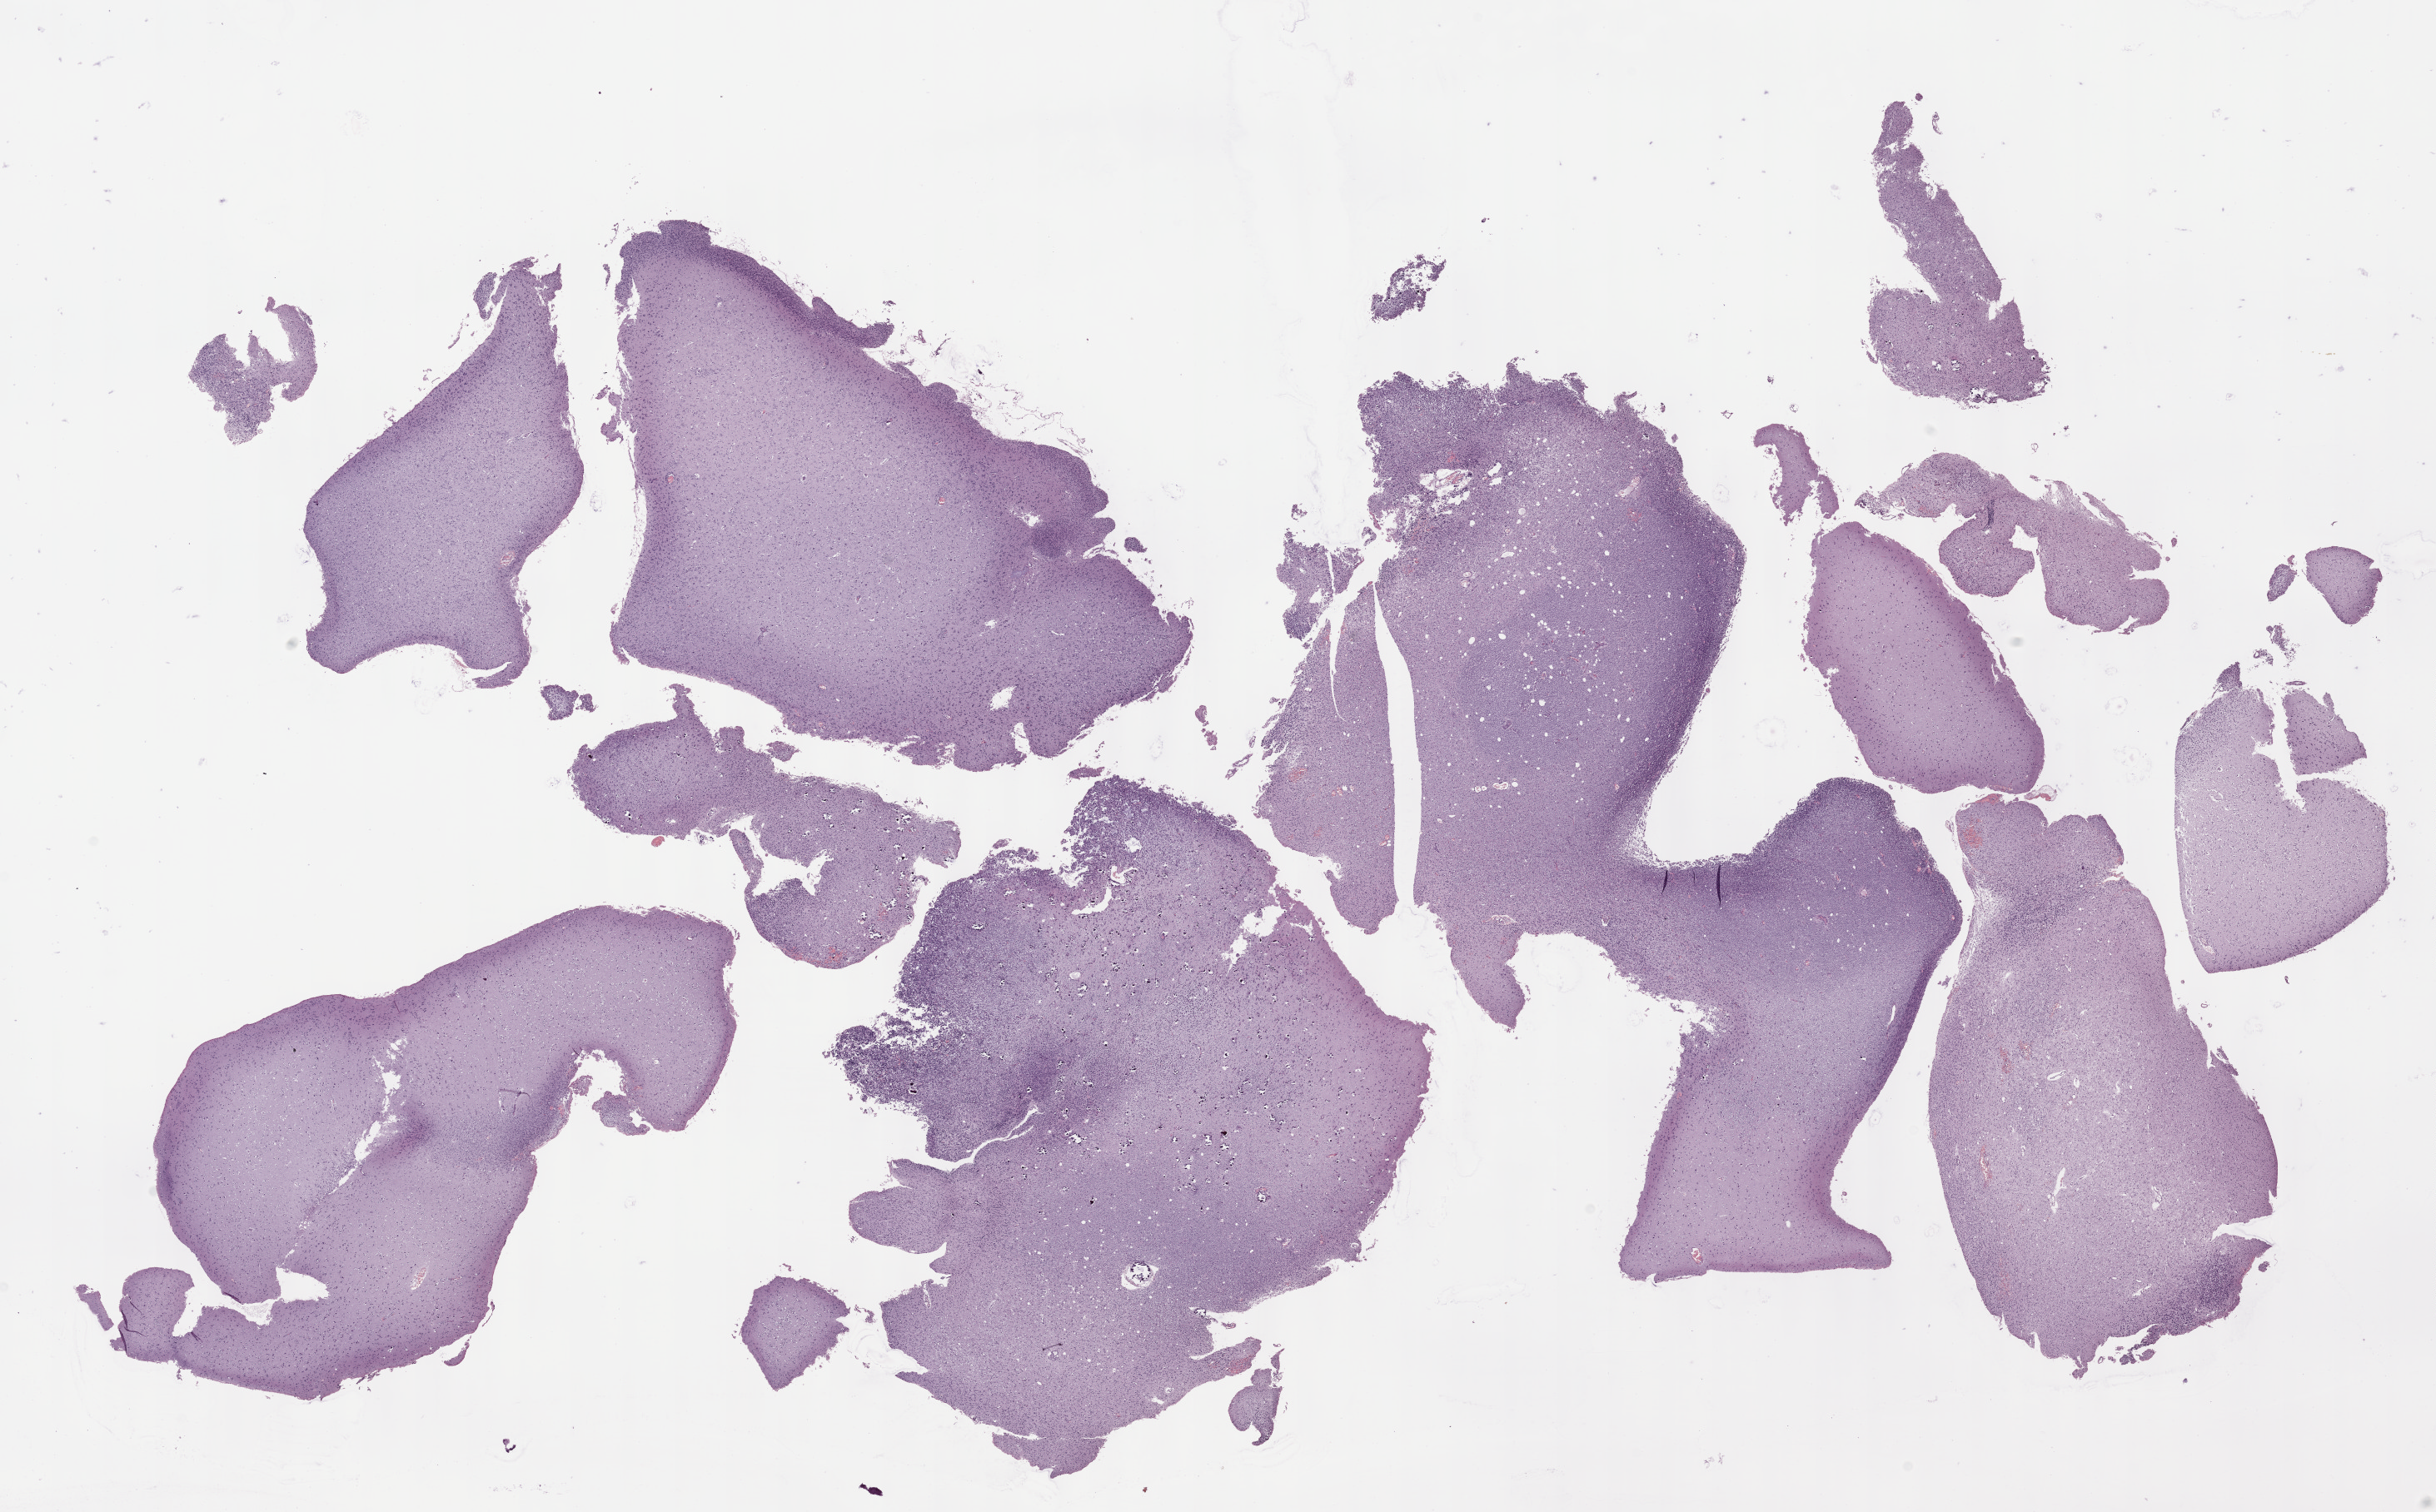
Whole-slide histology image, Hematoxylin and eosin (H&E) stained — a low-resolution overview of the entire scanned area, about 23.6 x 14.7 mm, FFPE section, brain, primary tumour sample. Female patient; age at initial diagnosis 64 years. Histologic grade: G3 (poorly differentiated).
Diagnosis: Oligodendroglioma, anaplastic (cerebrum).